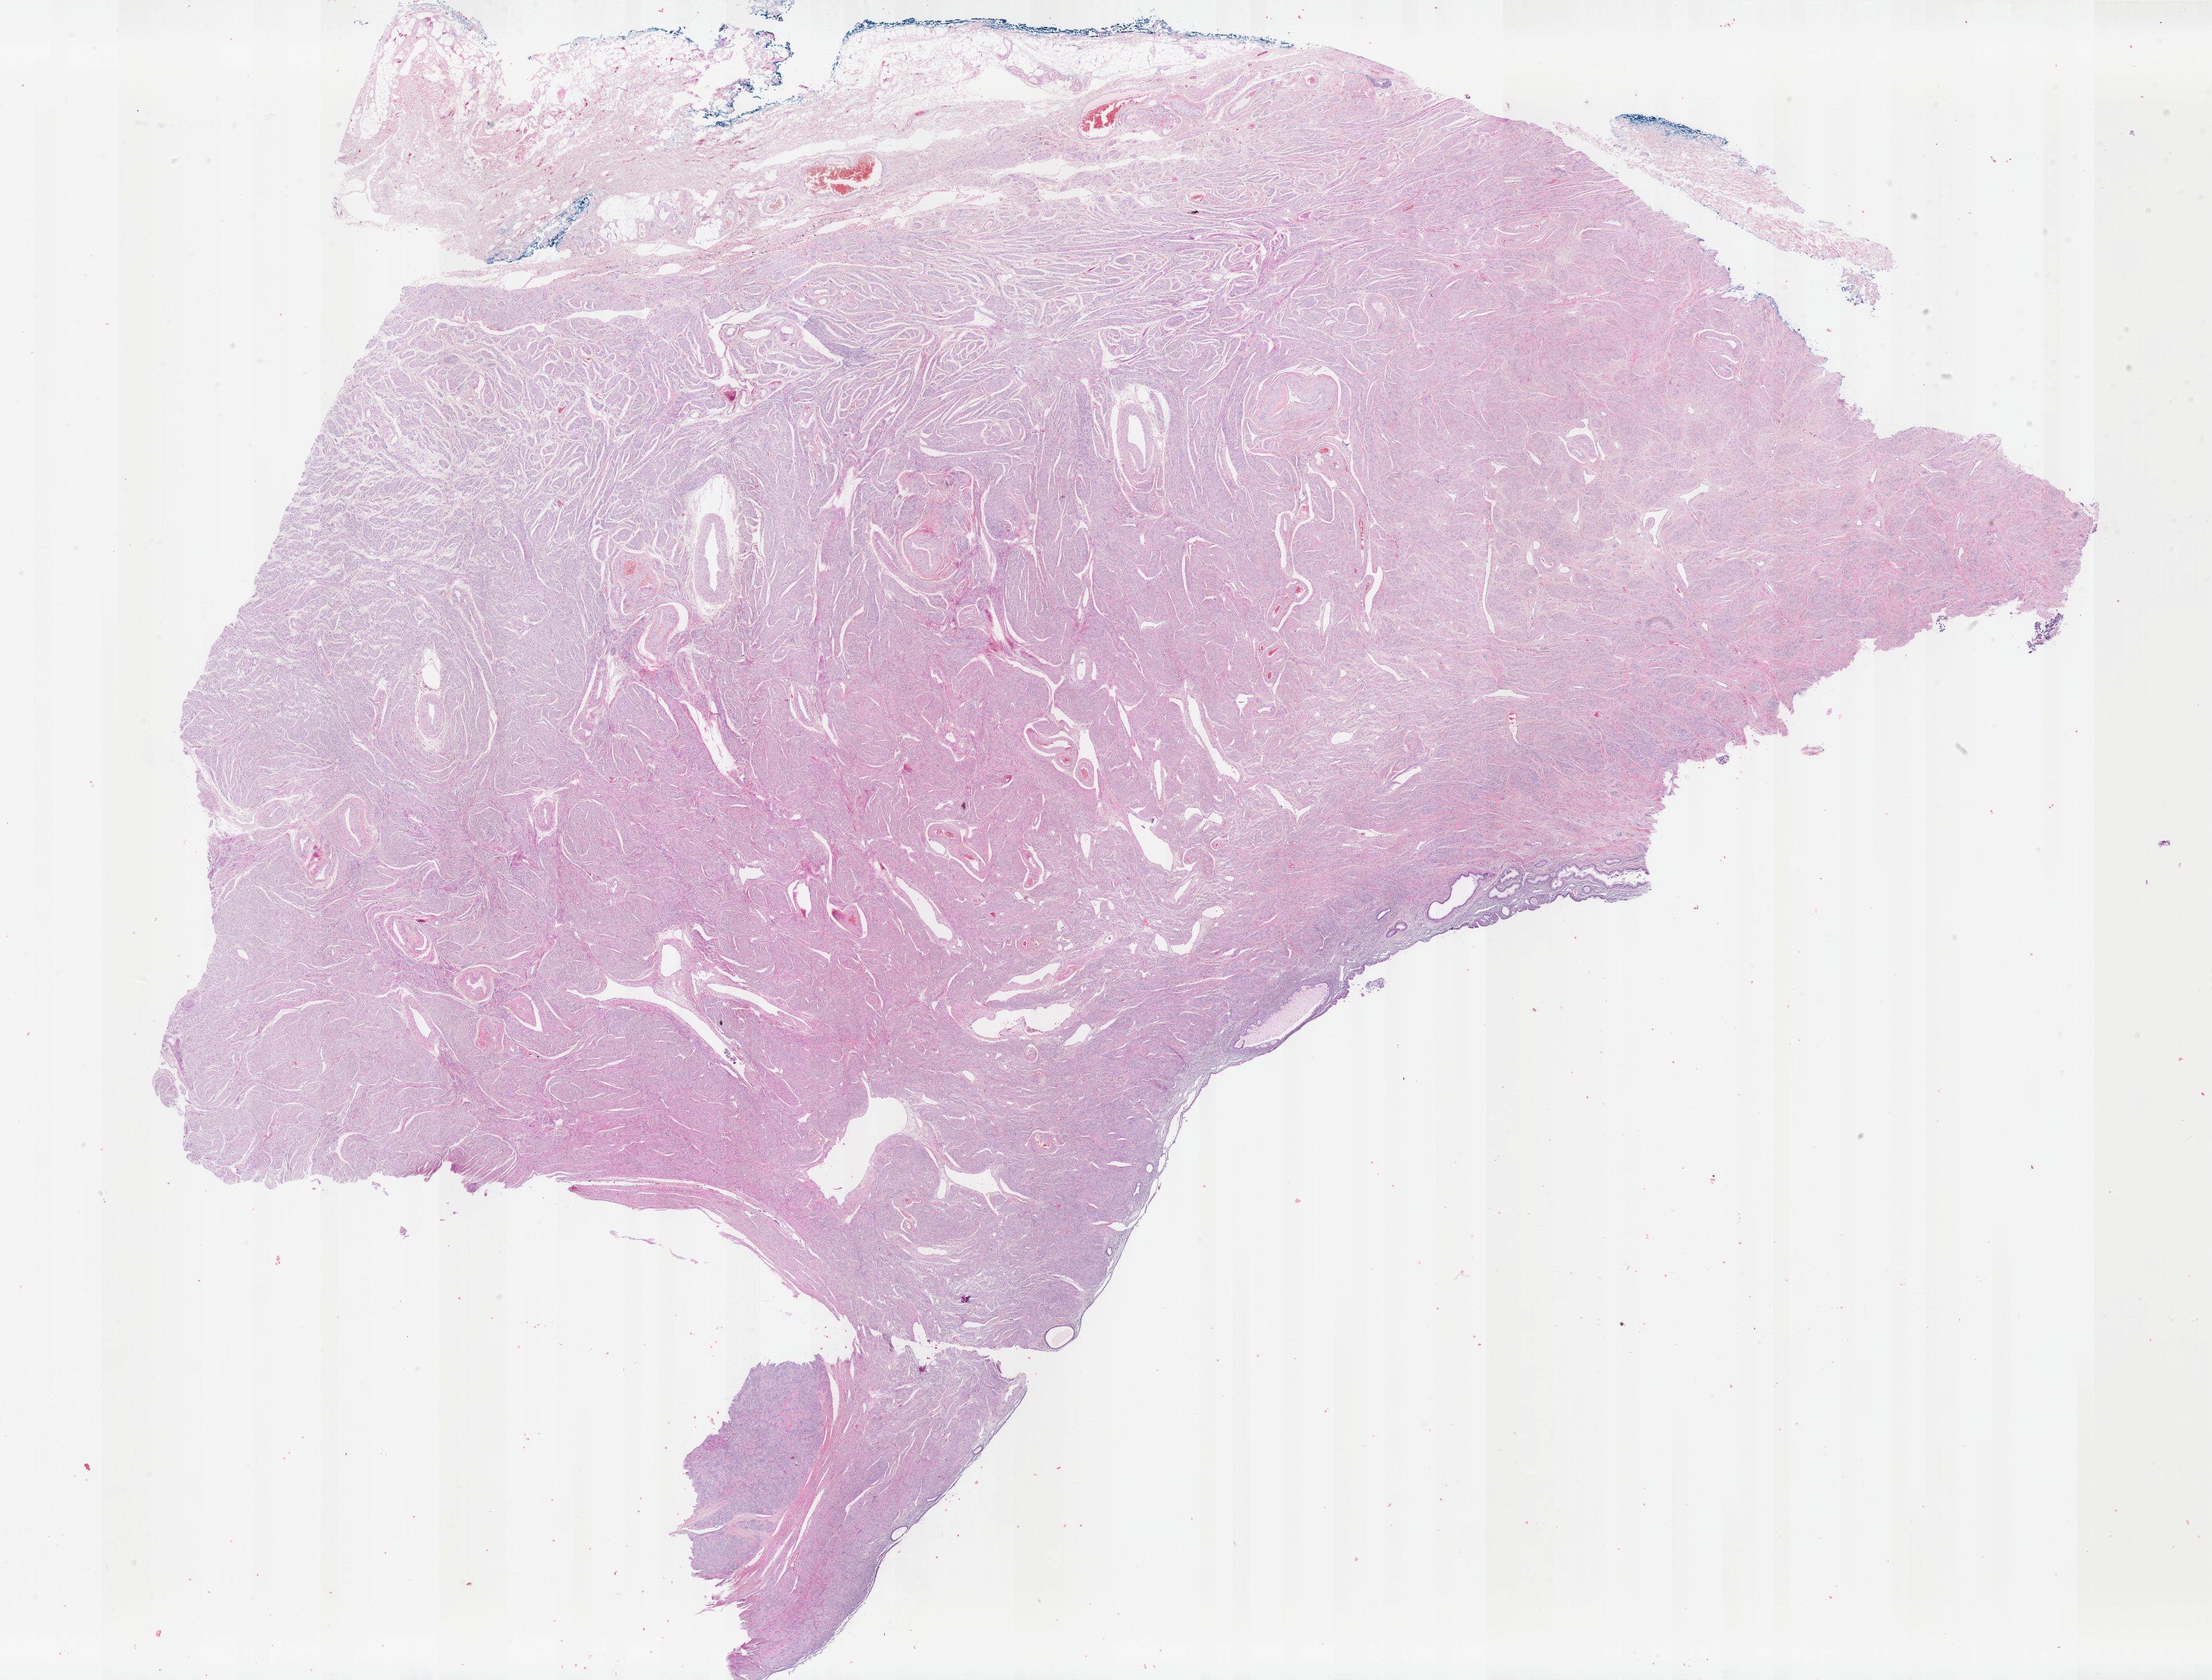
Digitized Hematoxylin and eosin (H&E) stained tissue section (whole slide) — a low-resolution overview of the entire scanned area, about 30.9 x 23.5 mm (slide scanned at 40x). FFPE section. Primary tumour sample from the uterus. Female patient; age at initial diagnosis 65 years. Histologic grade: G3 (poorly differentiated).
Lymph nodes positive (case pathology): 0 of 7 examined. Histologic diagnosis: Adenocarcinoma, NOS (endometrium). FIGO stage: IVB.